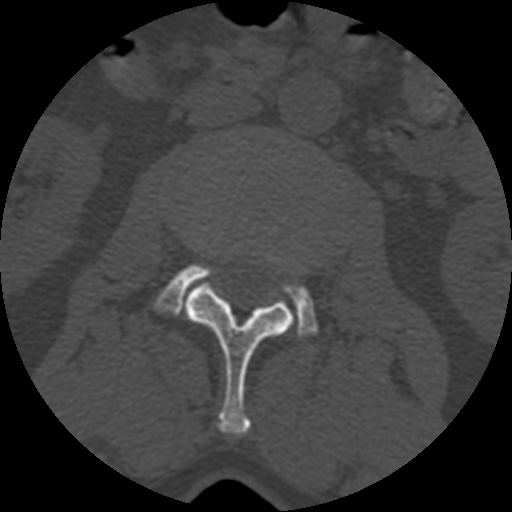
CT including the spine, one axial slice. Slice 324 of 399 in the series (ordered by position). Reconstruction kernel STANDARD. Bone window (W 1800 / L 400 HU). 1.25 mm slice thickness. 512 × 512 image matrix, field of view 160 × 160 mm. Patient age 71 years. Case-level facts recorded for this patient, not image findings: primary cancer: prostate.
Outlined on this slice (semi-automatically segmented with operator editing):
- L2 vertebra: bounding box (x1, y1, x2, y2) in pixels: (182, 283, 295, 435)
- L3 vertebra: (154, 264, 317, 337)